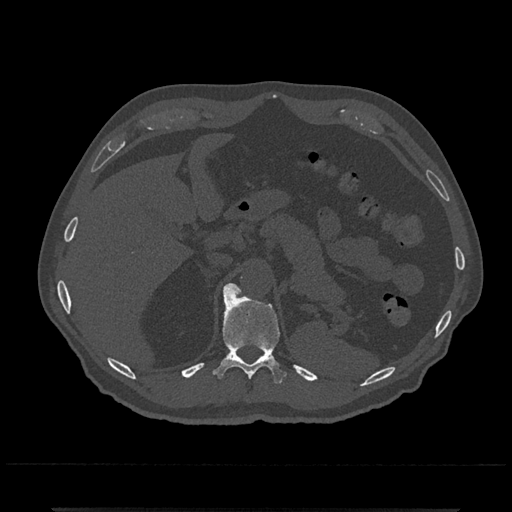
CT including the spine, one axial slice. 120 kVp. Bone window (W 1800 / L 400 HU). 512 × 512 image matrix. Patient: male, 67 years. Case-level facts recorded for this patient, not image findings: primary cancer: prostate.
Structures marked on this image (semi-automatically segmented with operator editing):
- T11 vertebra: bounding box <213,284,286,384> (left, top, right, bottom; pixels)
- T12 vertebra: <225,284,241,292>